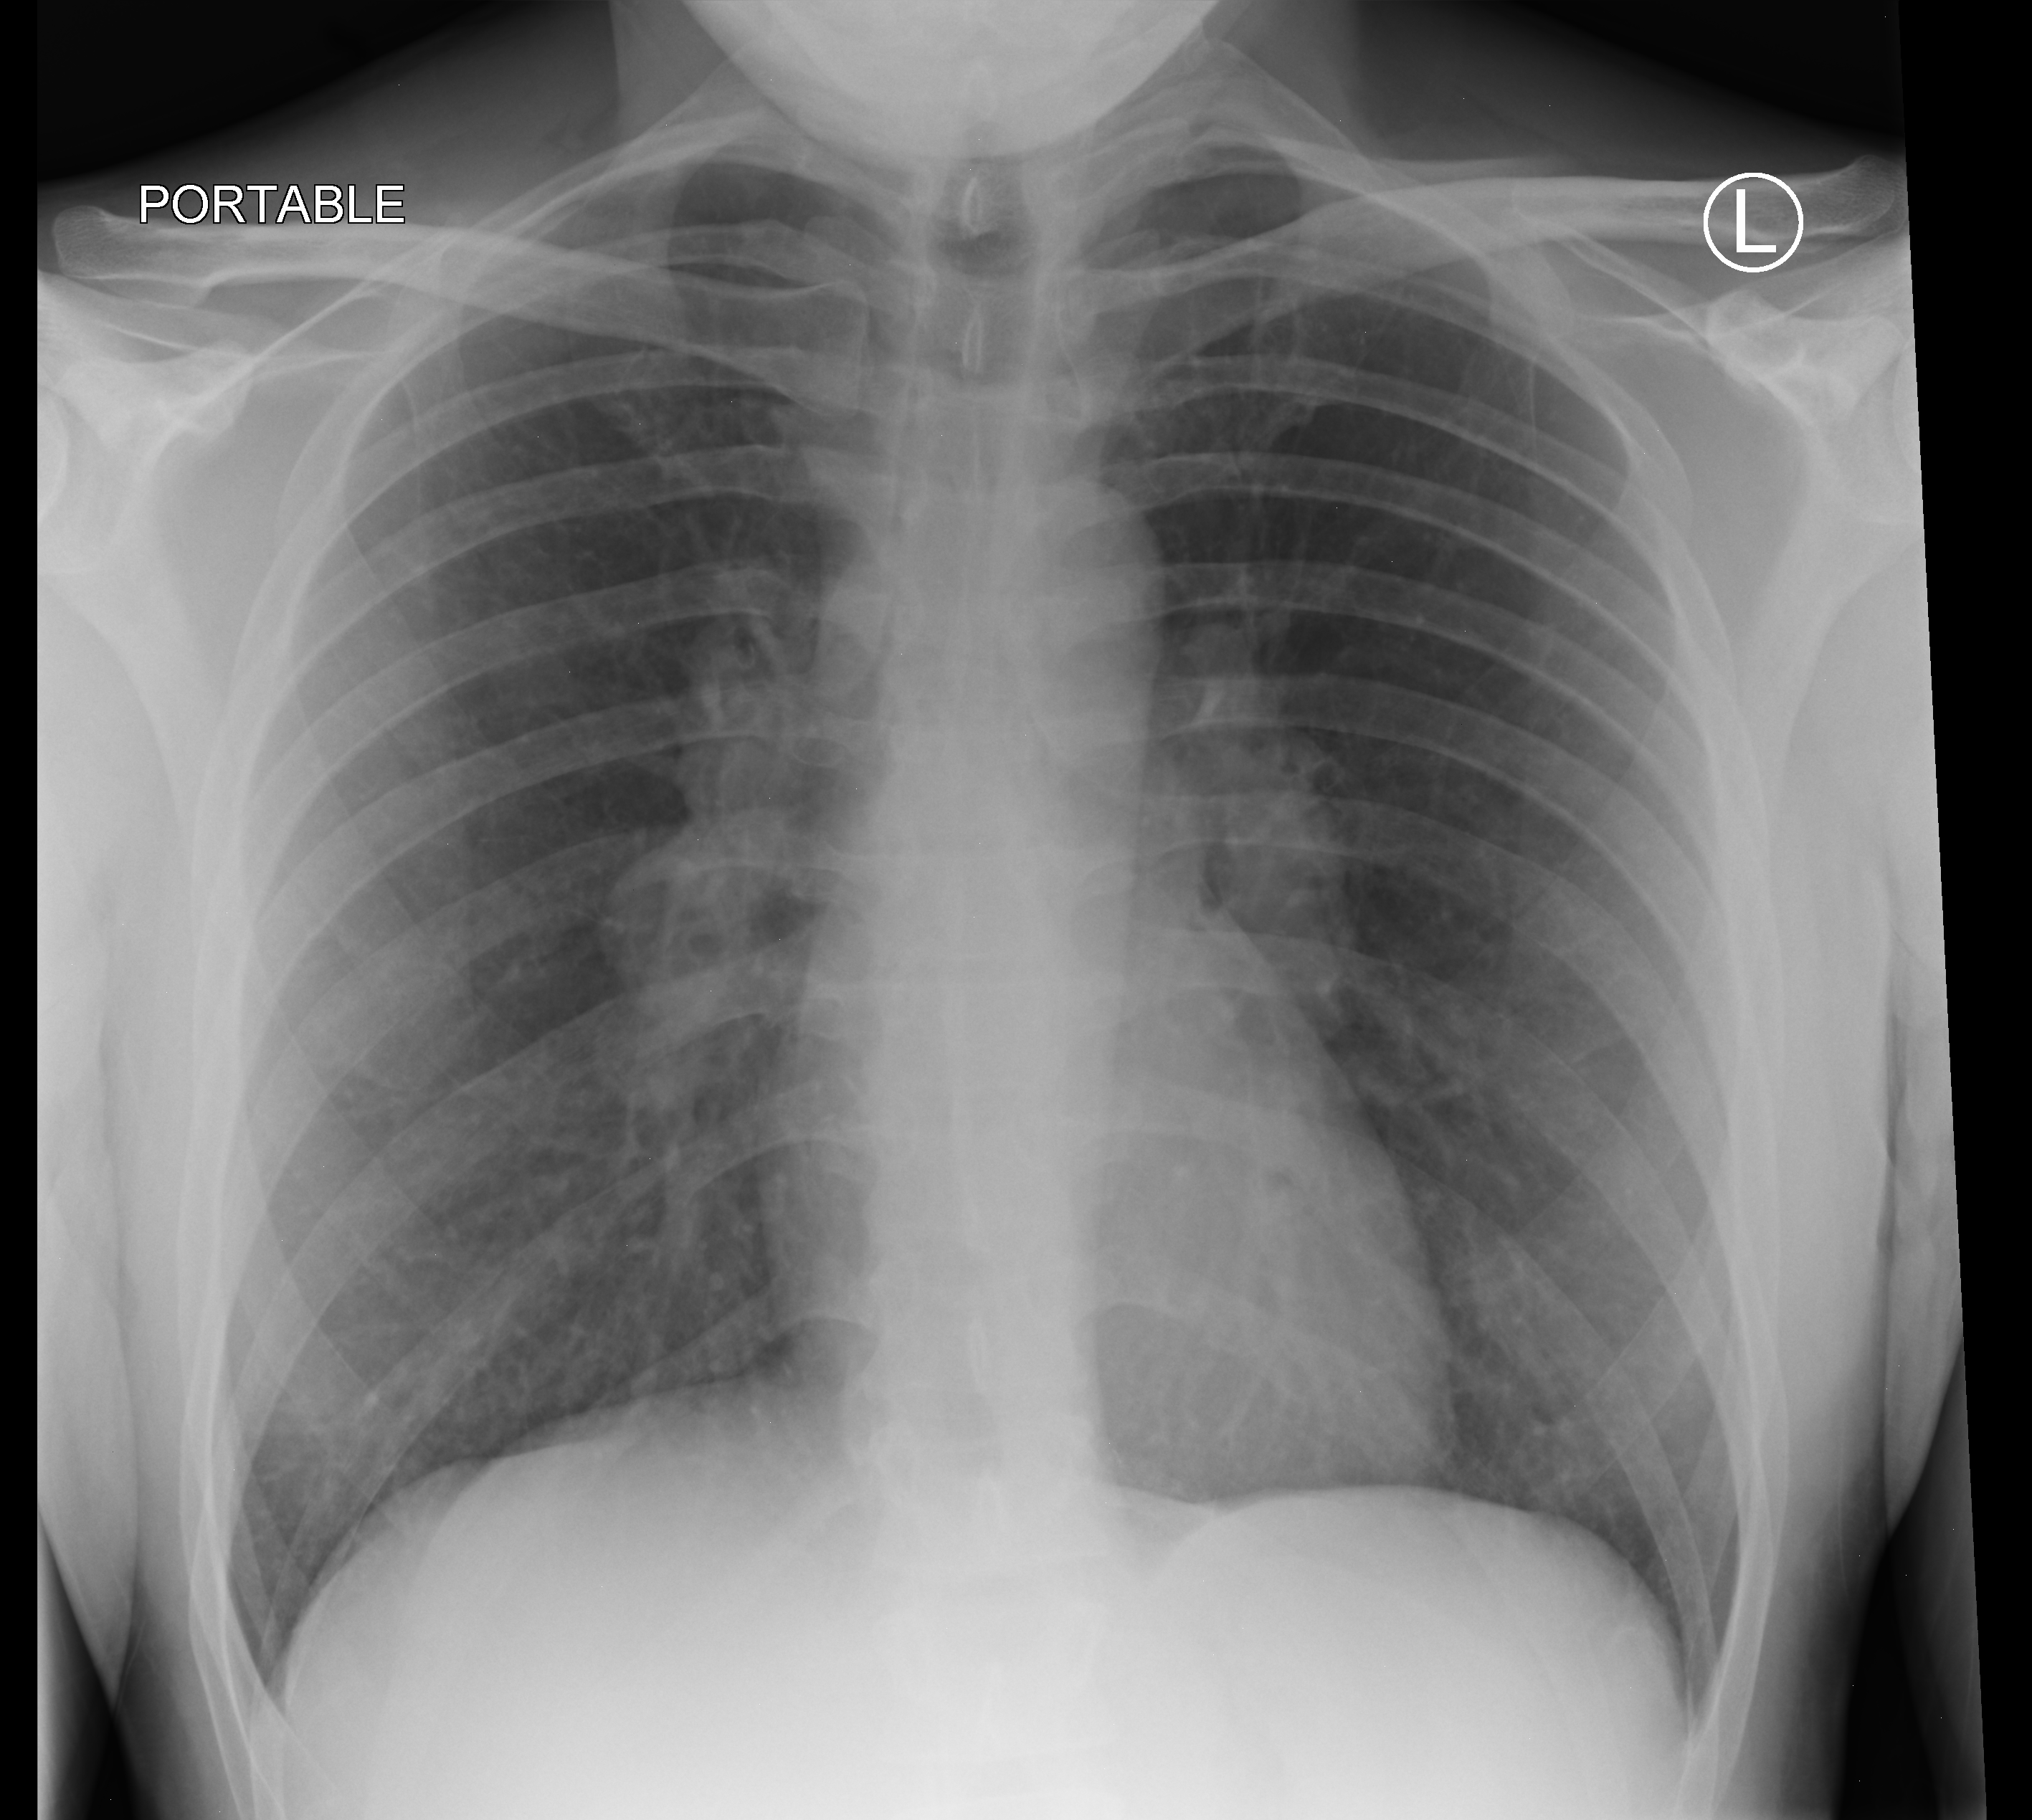
Bedside chest radiograph (computed radiography); anteroposterior (AP) projection. Patient hospitalised with COVID-19; male, aged 18–59 years.
Admission-level facts for this patient (not findings on this image; timing relative to this image not recorded): length of hospital stay: 1 day.